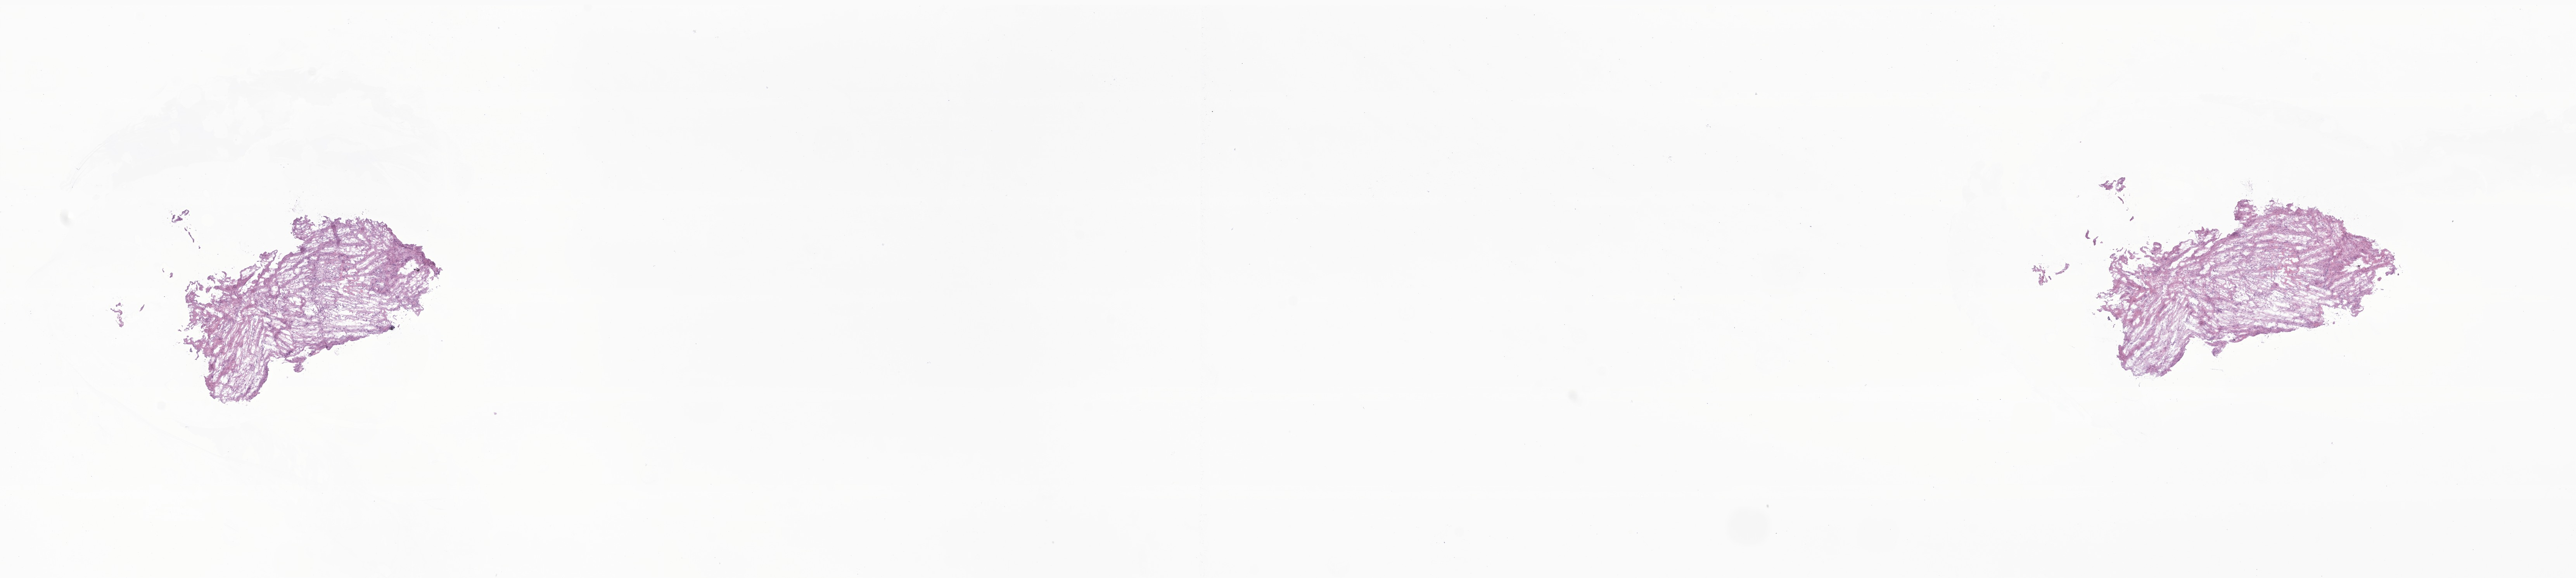
Haematoxylin and eosin whole-slide image of tumor tissue from the soft tissue of upper extremity, shown as a low-resolution overview of the whole scanned area (about 28.0 x 6.3 mm), frozen section (OCT-embedded). Patient: male, age 285 months (23 years 9 months).
• diagnosis: Sclerotic fibroma